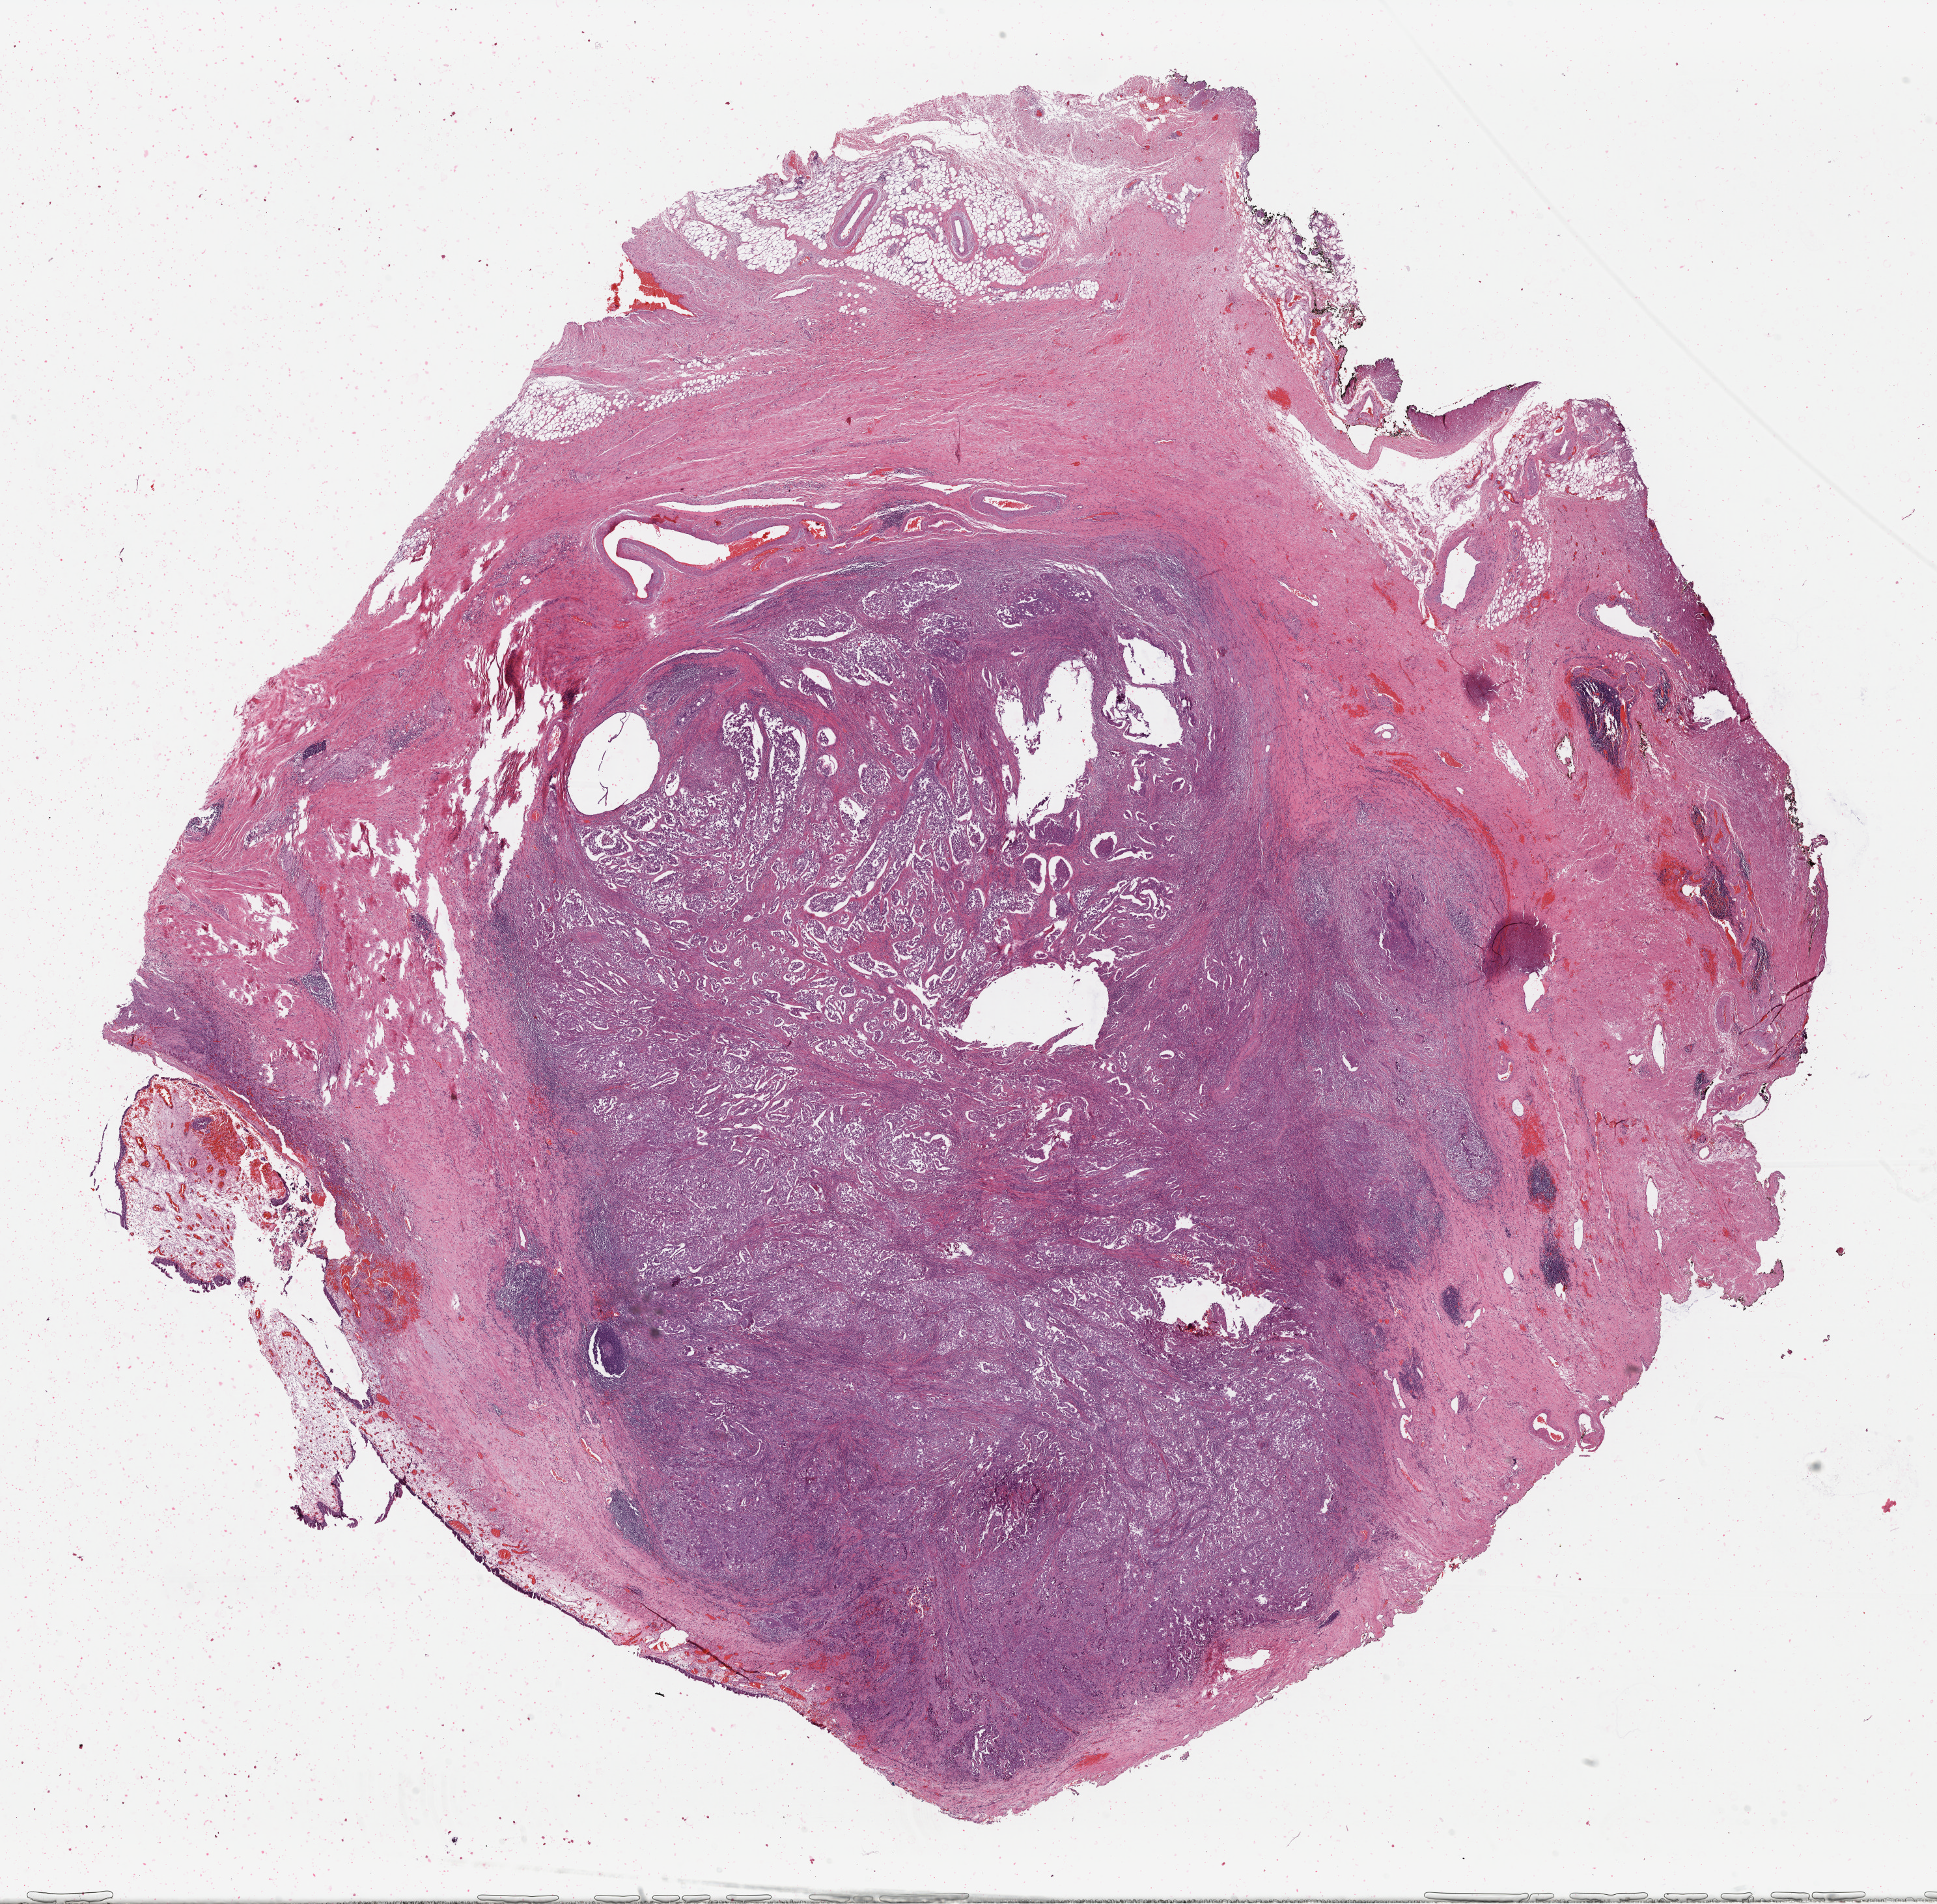
Digitized Hematoxylin and eosin (H&E) stained tissue section (whole slide) — low-resolution overview of the scanned area, about 23.4 x 23.0 mm (from a 40x scan). Formalin-fixed paraffin-embedded (FFPE) diagnostic section. Bladder, primary tumour sample. Male, age 87 years at initial diagnosis.
Histologic diagnosis: Transitional cell carcinoma.